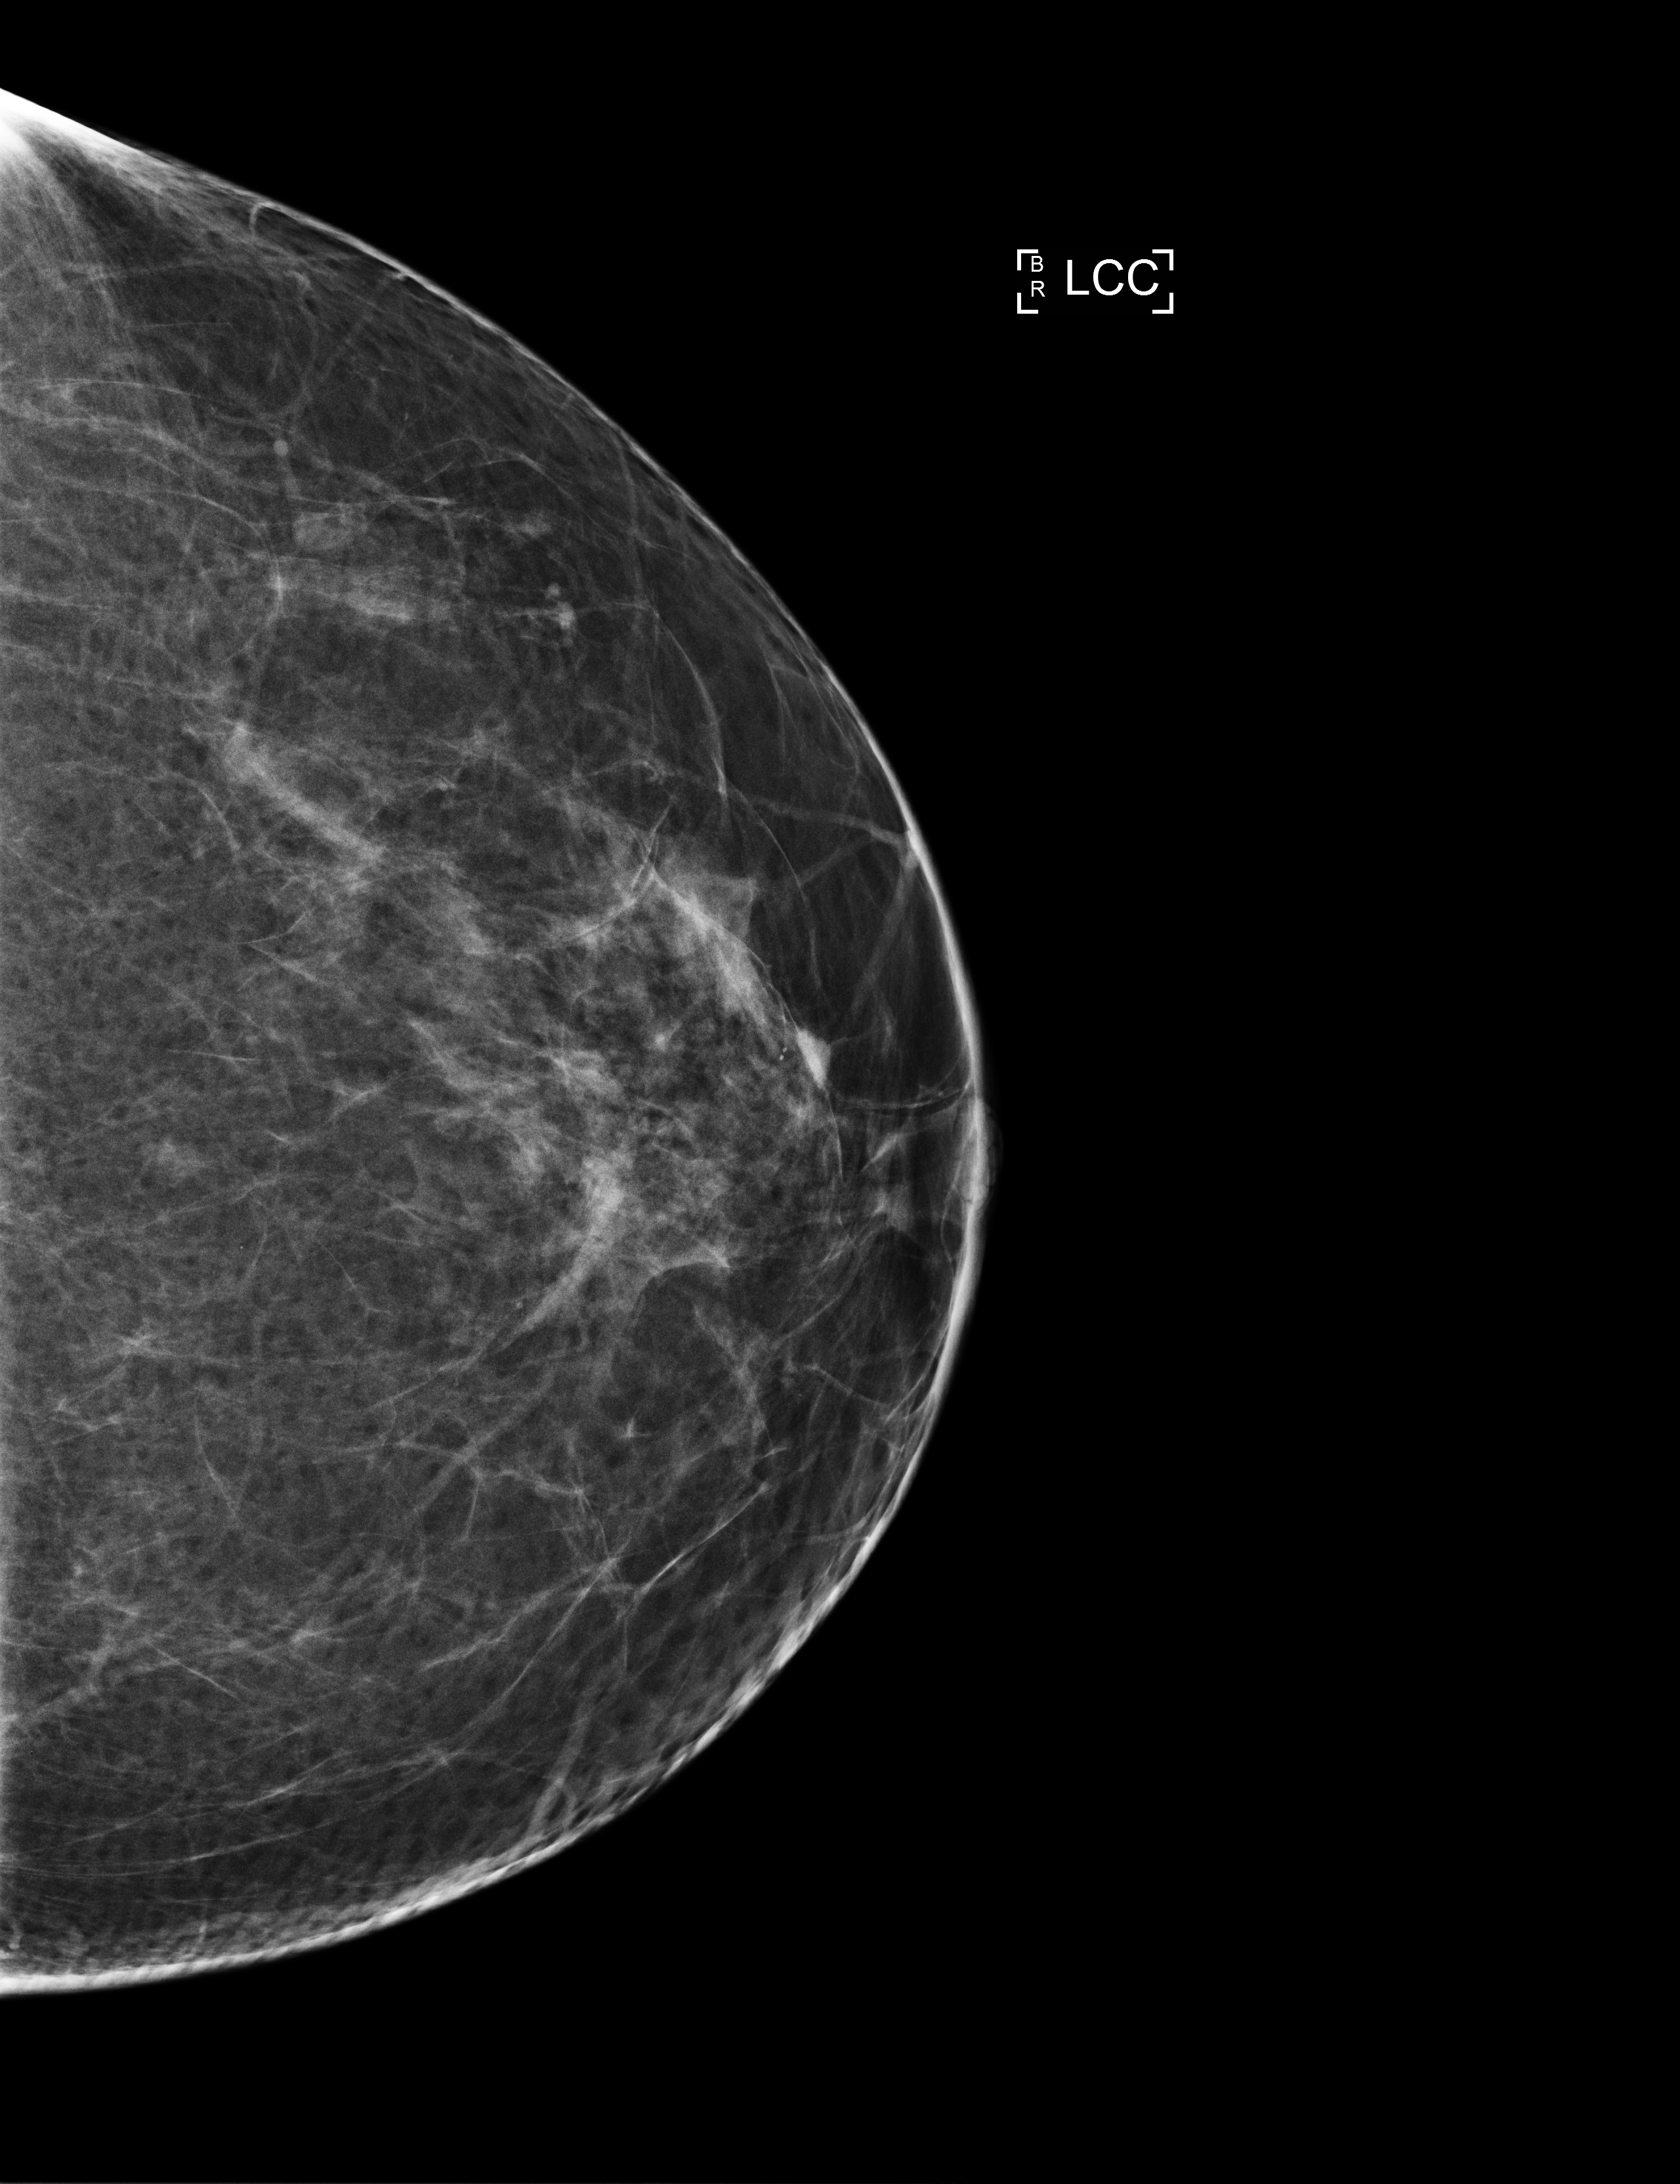
Digital mammogram (FFDM); left breast; craniocaudal (CC) view; annual screening mammography examination; compressed breast thickness 96 mm. Patient: female, 44 years.
BI-RADS breast density category at the screening exam (both breasts, scale 1–4): 2. Final BI-RADS category for the screening round (tomosynthesis exam, both breasts): category 2. Recall: no recall after this screen.